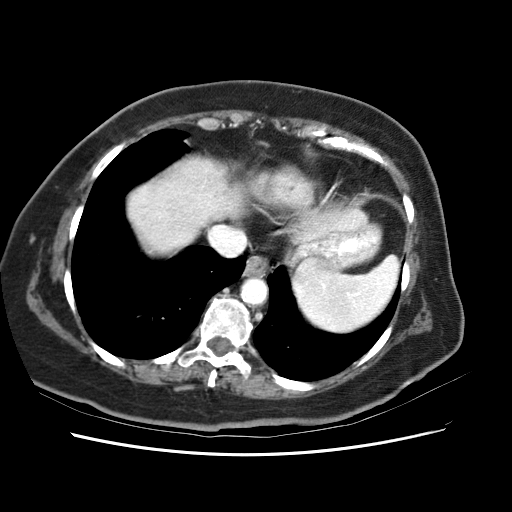
Contrast-enhanced abdominal CT (liver protocol), one axial slice. Position 56 of 62 along the scan axis. 120 kVp. Soft-tissue window (W 400 / L 40 HU). 2.5 mm slice thickness. 512 × 512 image matrix. Case-level facts recorded for this patient, not image findings: diagnosis: hepatocellular carcinoma (patient treated with transarterial chemoembolisation; whether this scan precedes or follows treatment is not stated here); TNM stage (as recorded): Stage-I; Child-Pugh class: B; tumour nodularity: uninodular; tumour size: 5.3 cm.
Annotated regions visible in this slice (semi-automatically segmented with operator editing):
- abdominal aorta: bounding box <242,278,267,306> (left, top, right, bottom; pixels)
- liver parenchyma outside the tumour (the mass and vessels are separate outlines, so this box may not span the whole liver): <136,166,222,235>